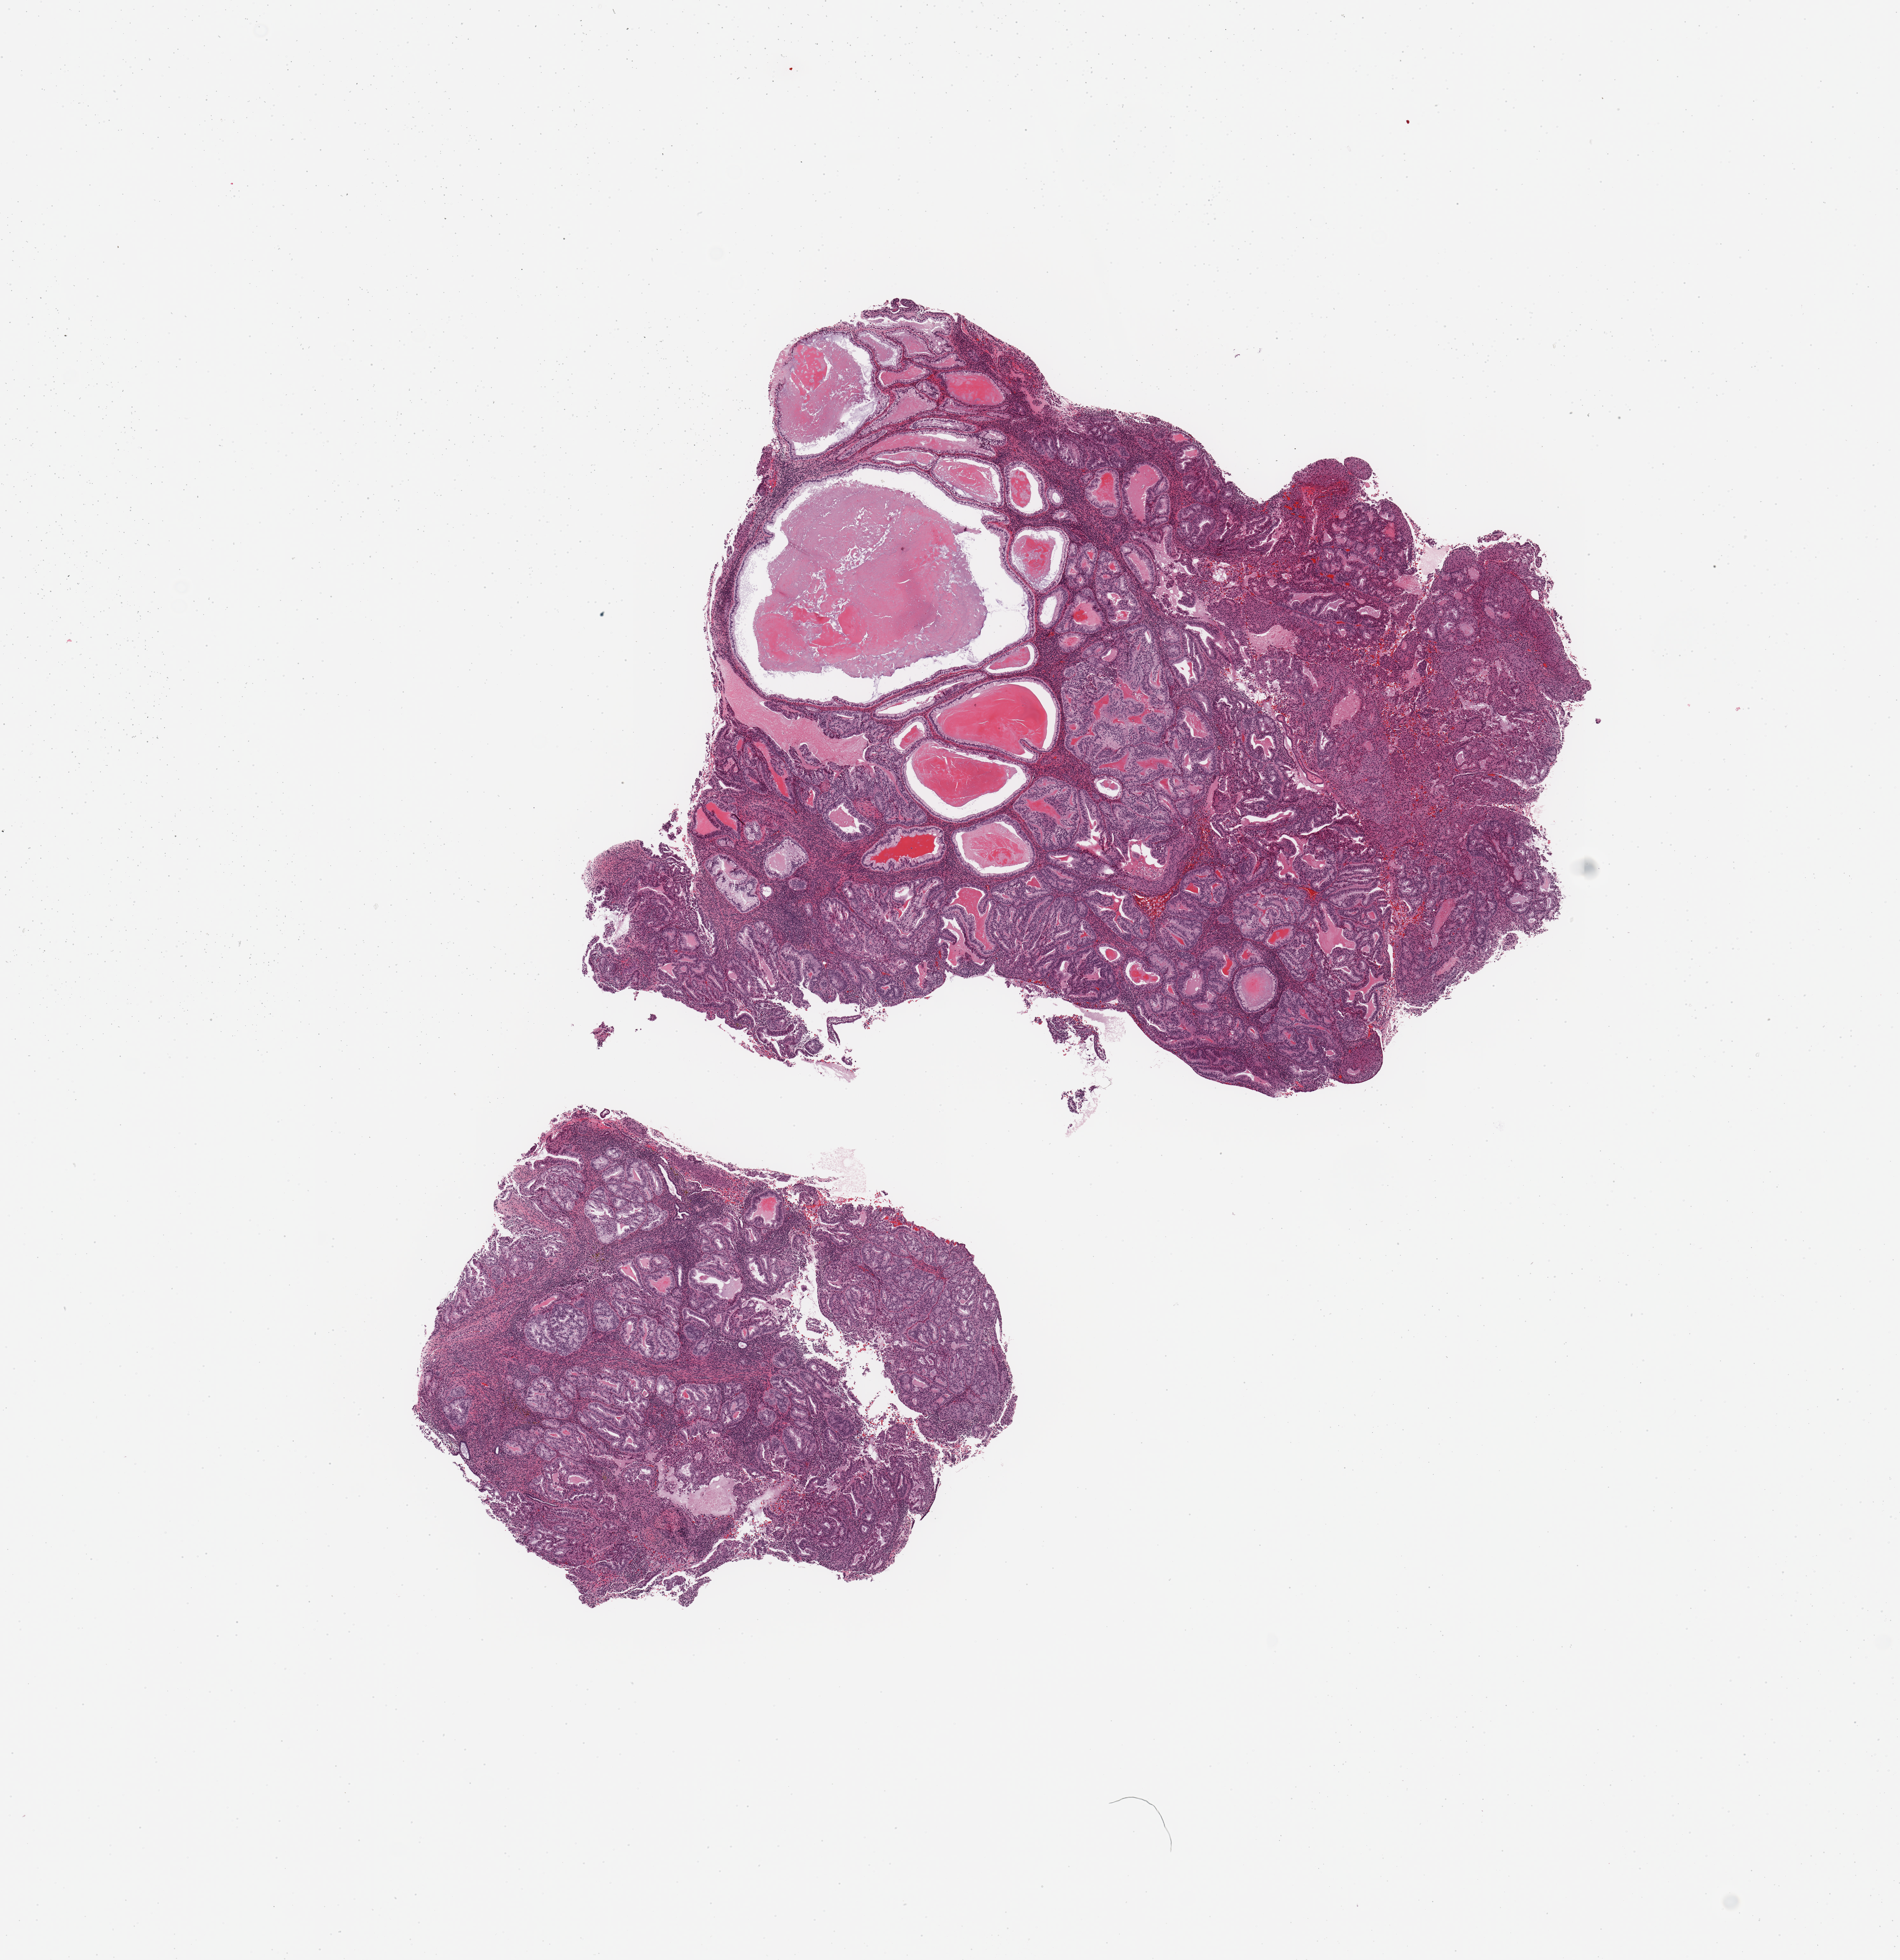
Digitized Hematoxylin and eosin (H&E) stained tissue section (whole slide) — shown as a low-resolution overview of the whole scanned area (about 11.8 x 12.2 mm). Uterus, tumour tissue. Female, 68 y/o. Histologic grade: G1 (well differentiated).
Histologic diagnosis: Endometrioid adenocarcinoma, NOS. AJCC pathologic stage: I.